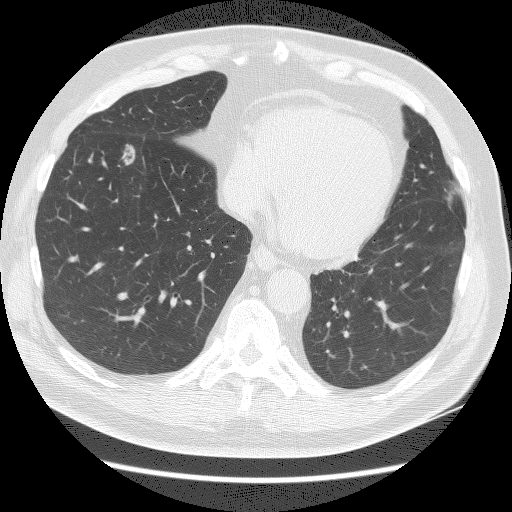
Axial slice from a low-dose chest CT screening exam, baseline annual screen, lung window (W 1500 / L -600 HU), 2.5 mm slice thickness. Male participant, aged 65 years at enrolment. Current smoker at enrolment.
Lesion marked by an expert reader, bounding box [x1, y1, x2, y2] px = [103, 134, 151, 172]. The screening reader recorded 3 non-calcified nodules or masses ≥4 mm on this exam (right lower lobe, right middle lobe, left upper lobe); which of them this box marks is not recorded. Official screen result: positive, change unspecified: nodule(s) >= 4 mm or enlarging nodule(s), mass(es), or other non-specific abnormalities suspicious for lung cancer. Lung cancer was diagnosed 132 days after this screen: adenocarcinoma, NOS, right lower lobe, poorly differentiated (G3), stage IA (AJCC 6th edition), 10 mm at pathology.